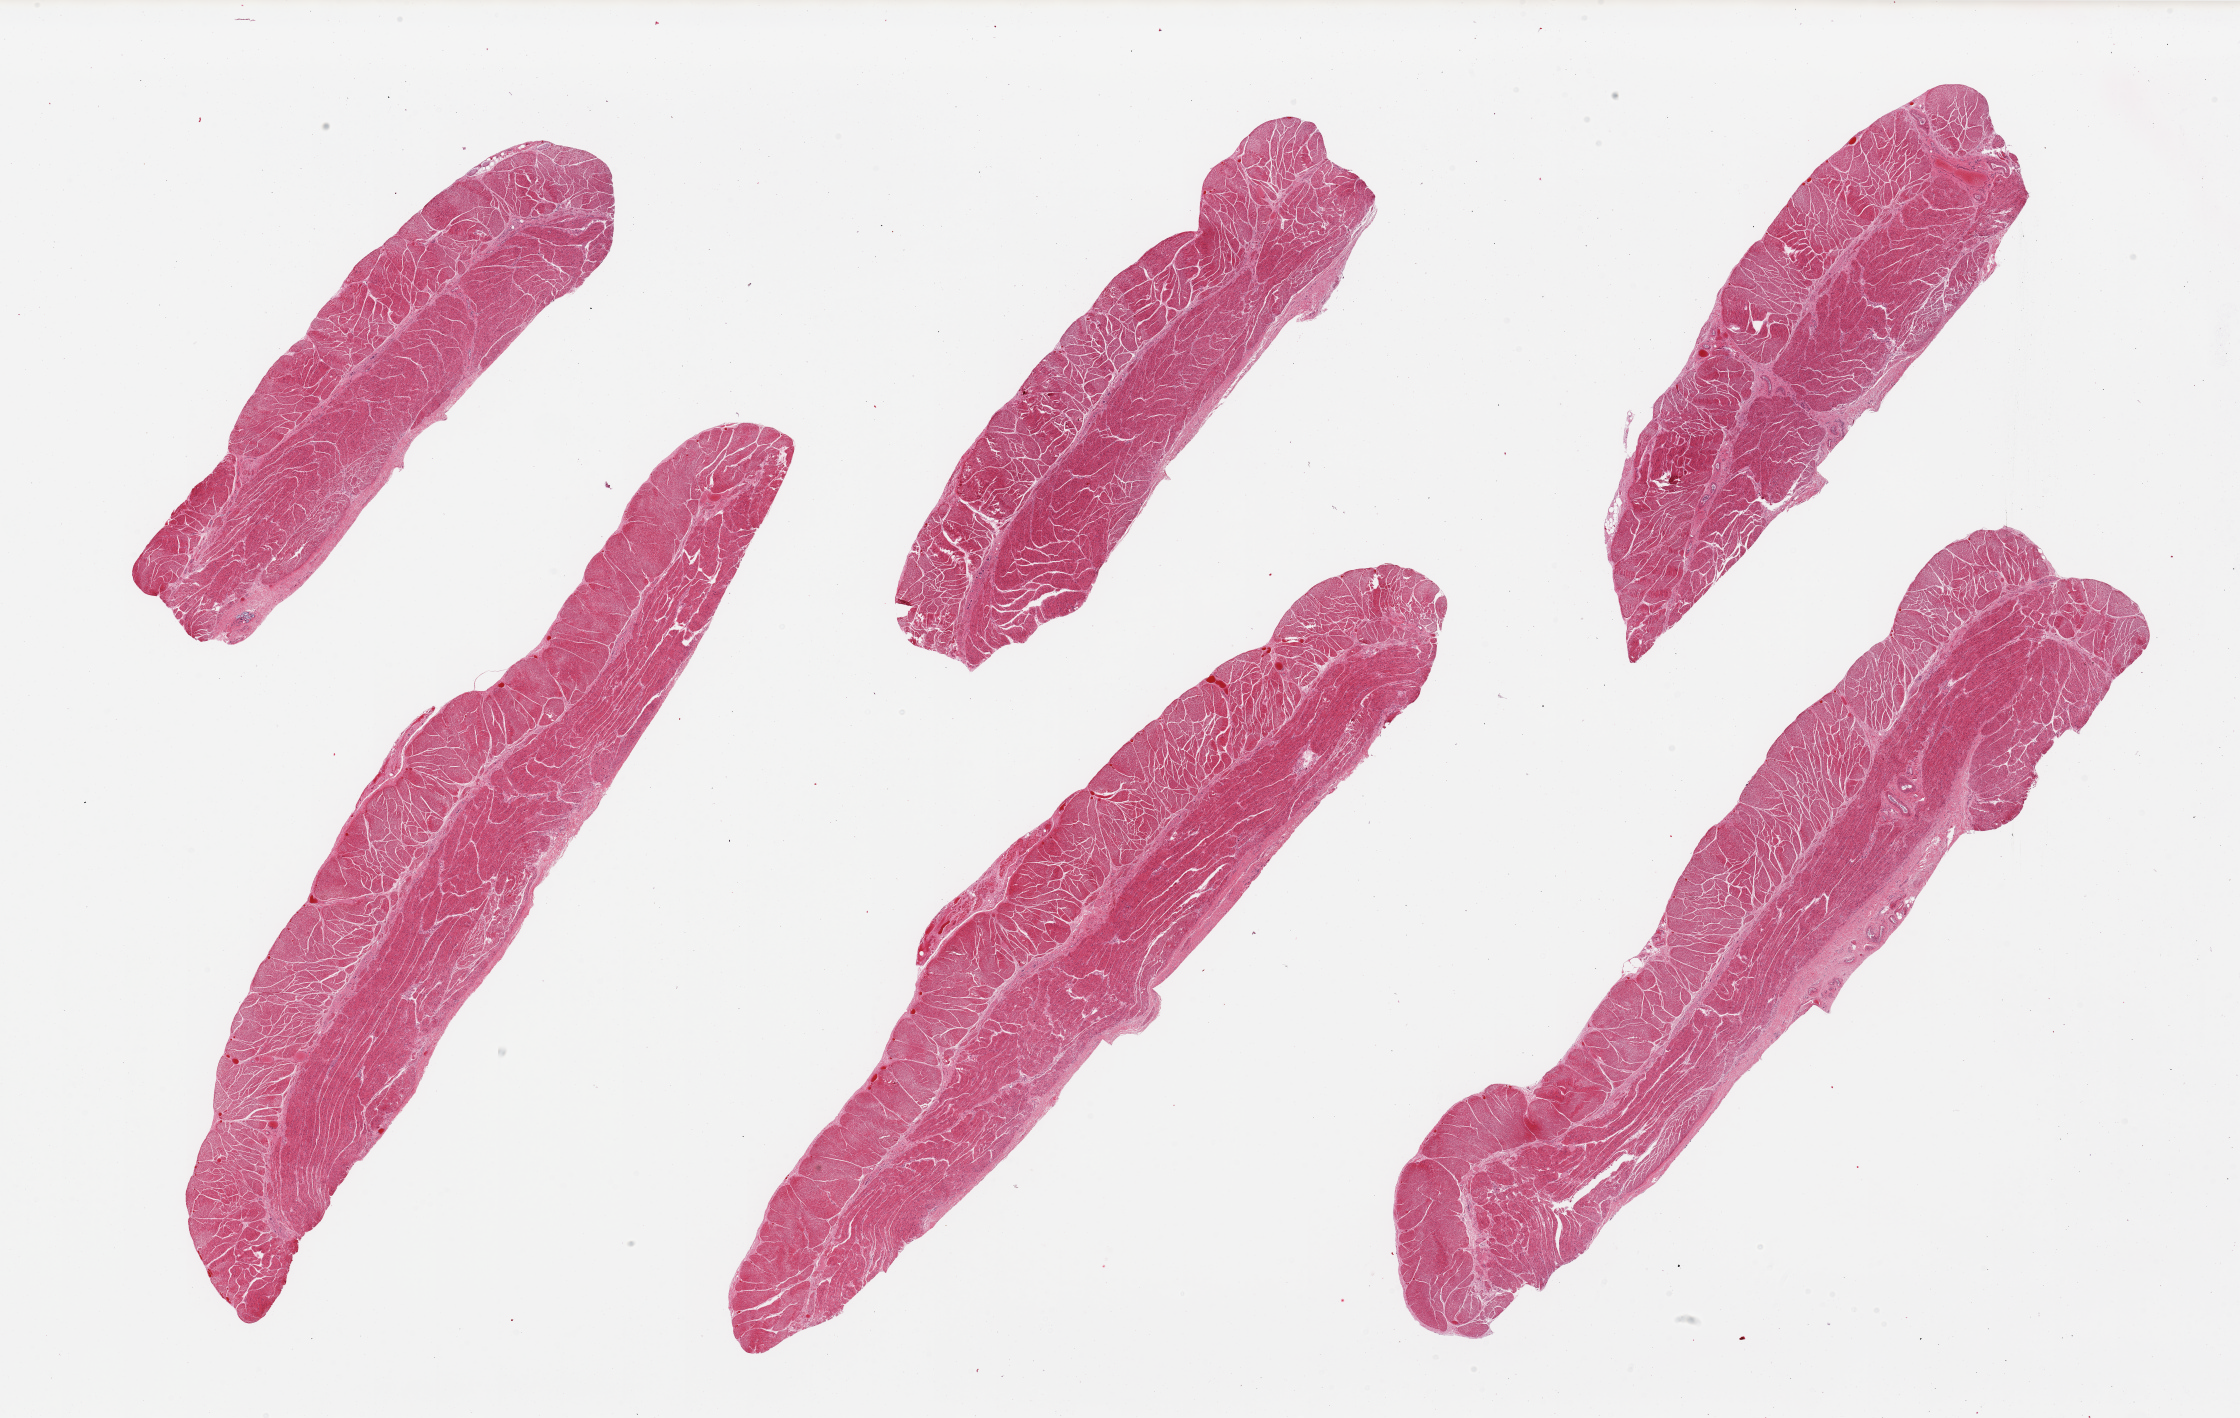
Digitized haematoxylin and eosin-stained section — shown as a low-resolution overview of the whole scanned area (about 35.4 x 22.4 mm, acquisition: 20x scan); PAXgene-fixed paraffin-embedded (PFPE) section; section of esophageal muscle (target tissue); donor tissue sample. Donor sex: male.
Review note (as recorded): 6 pieces; well dissected.